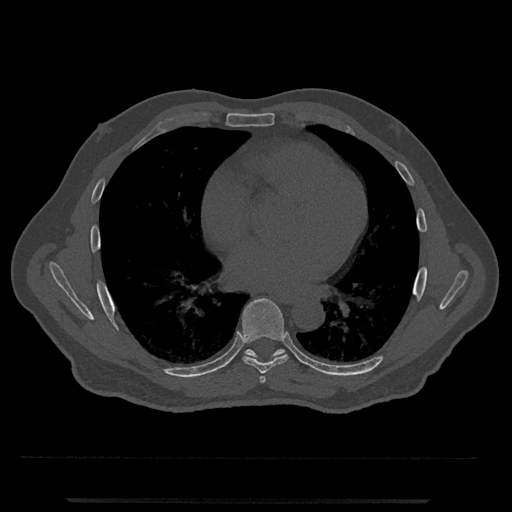
CT including the spine, one axial slice. Slice 668 of 797 in the series (ordered by position). Reconstruction kernel Br40s/3. 120 kVp. Bone window (W 1800 / L 400 HU). 0.5 mm slice thickness. 512 × 512 image matrix, field of view 419 × 419 mm. Male patient, age 63 years. Case-level facts recorded for this patient, not image findings: primary cancer: prostate.
Structures marked on this image (semi-automatically segmented with operator editing):
- T6 vertebra: bounding box [x1, y1, x2, y2] px = [259, 376, 266, 383]
- T7 vertebra: [241, 298, 289, 374]
- T8 vertebra: [244, 349, 286, 358]